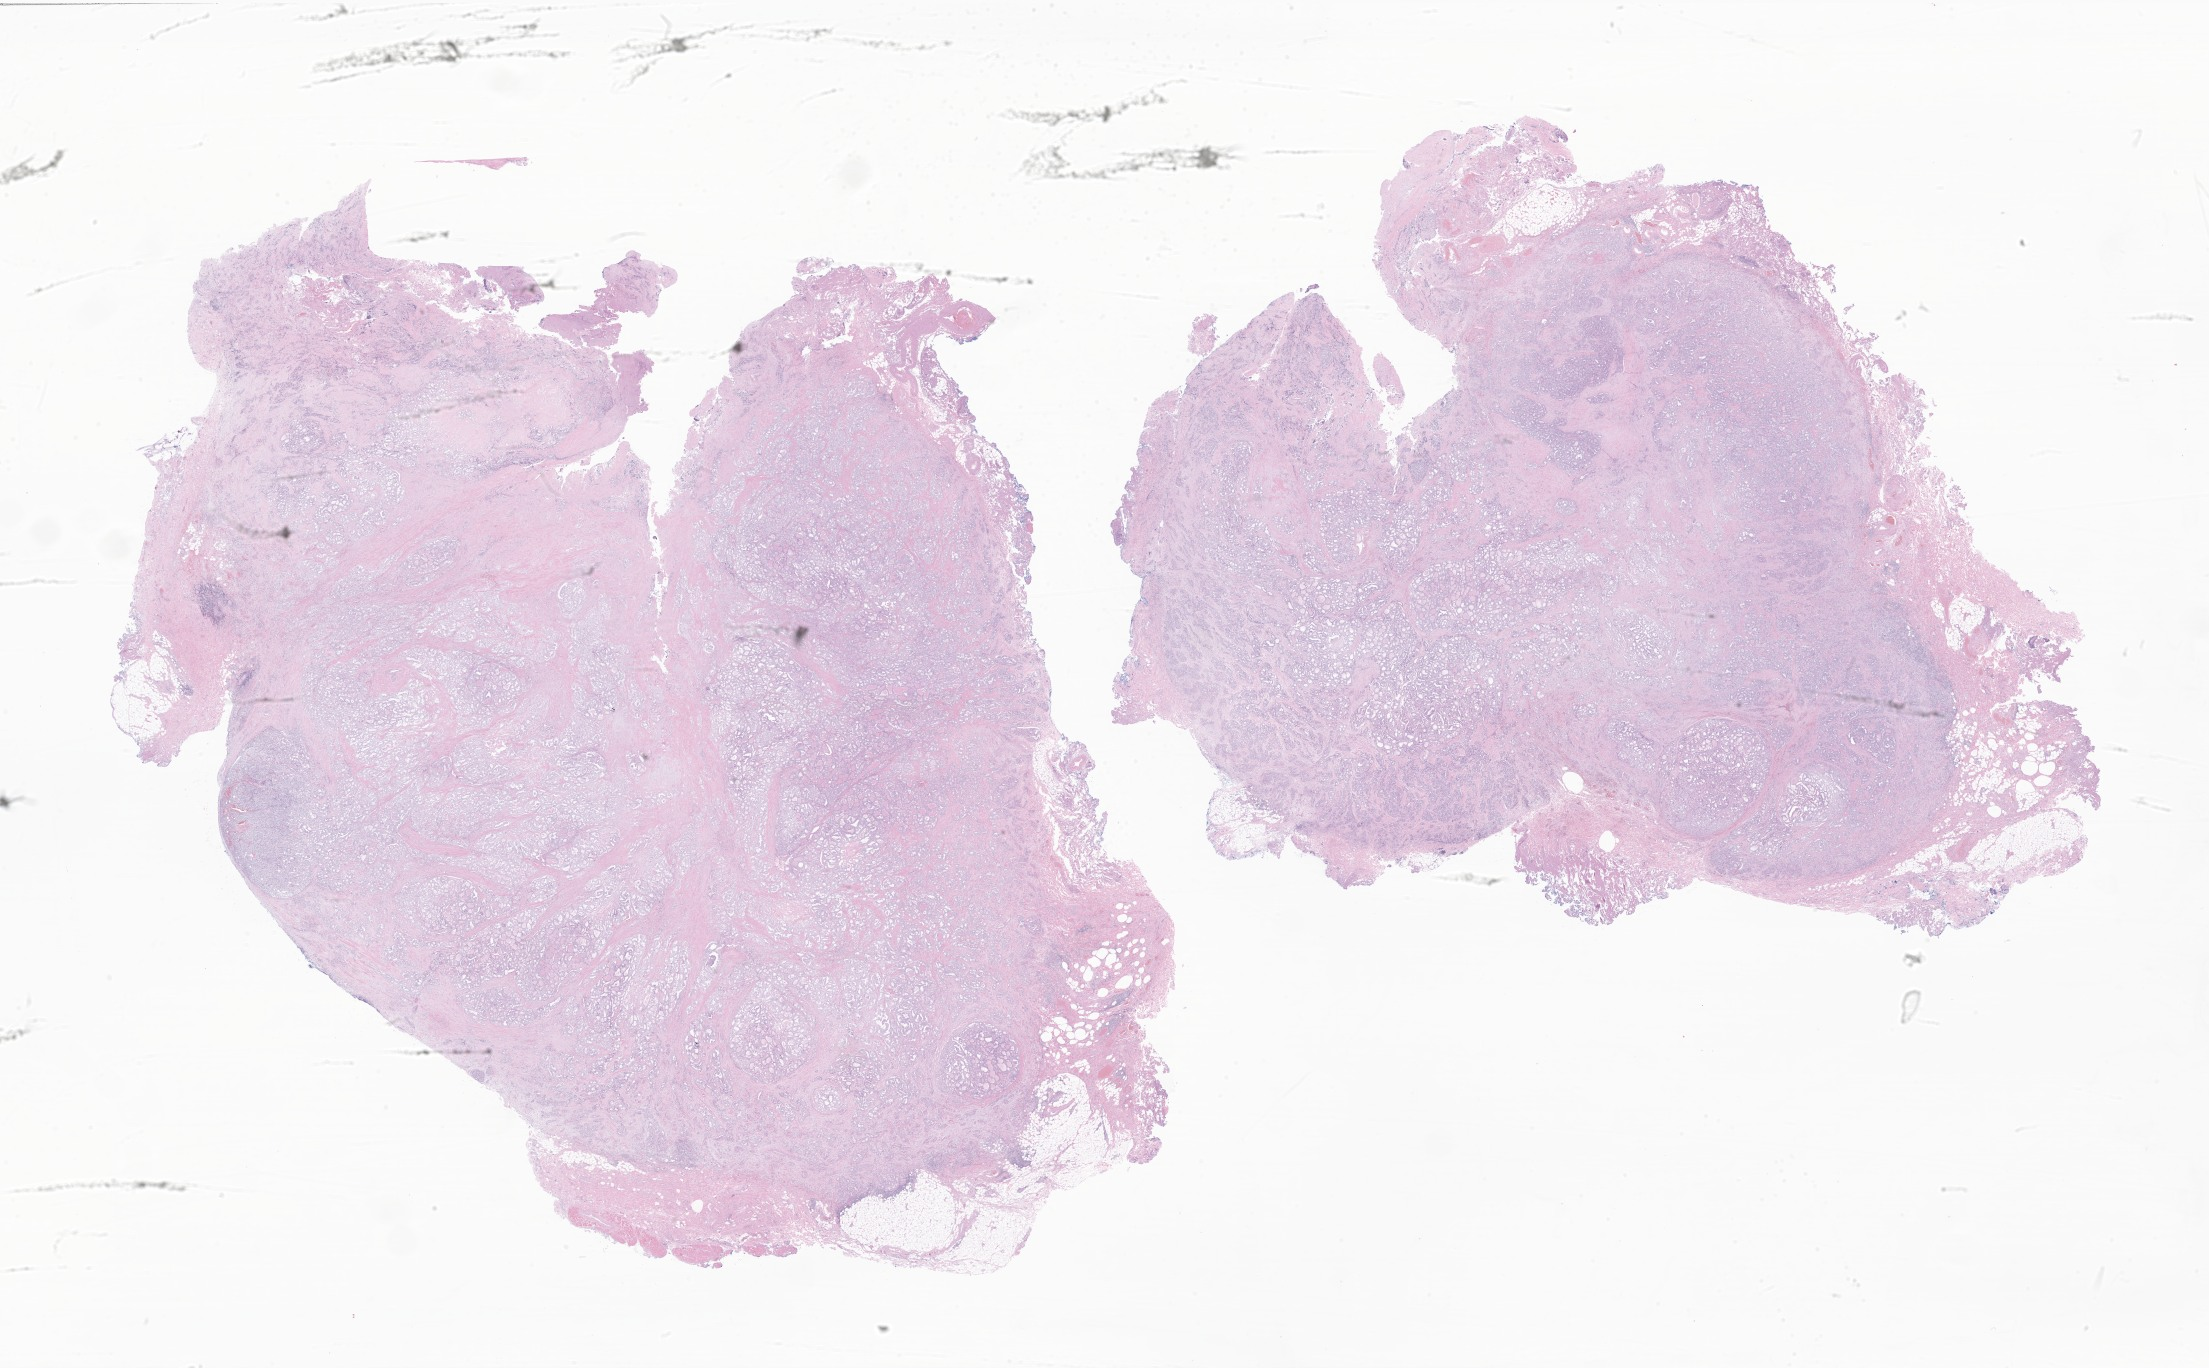
Haematoxylin and eosin whole-slide image of tumor tissue from the thyroid, shown as a low-resolution overview of the whole scanned area (about 37.3 x 23.1 mm). Formalin-fixed paraffin-embedded section. Patient male; age 102 months (8 years 6 months).
• diagnosis (ICD-O-3 morphology term): Papillary carcinoma, NOS